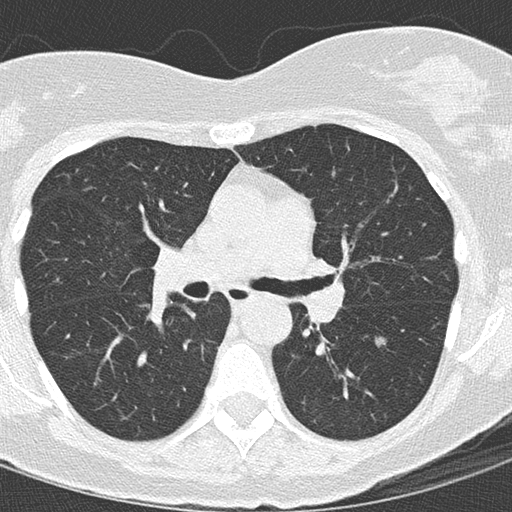
Axial slice from a low-dose chest CT screening exam. Baseline annual screen. Lung window (W 1500 / L -600 HU). 2 mm slice thickness. Lung (sharp) reconstruction kernel (B50f). Slice 59 of 145 in the series. 512 × 512 image matrix. Female, age 68 years at enrolment. Current smoker at enrolment.
Expert-annotated lung lesion, bounding box [x1, y1, x2, y2] px = [364, 318, 411, 368]. Reader record for this screening exam (exam-level; its link to the box is not recorded): non-calcified nodule or mass ≥4 mm, left lower lobe, 15 × 15 mm, mixed attenuation. Lung cancer was diagnosed 72 days after this screen: bronchiolo-alveolar adenocarcinoma, NOS, left lower lobe, stage IIIB (AJCC 6th edition), 12 mm at pathology.